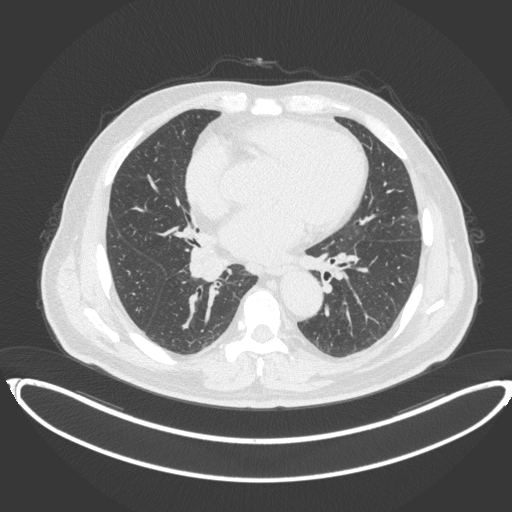
Chest CT, one axial slice. Position 192 of 383 along the scan axis. Reconstruction kernel B31f. 120 kVp. Lung window (W 1500 / L -600 HU). 1 mm slice thickness. 512 × 512 image matrix, field of view 448 × 448 mm. Male patient, age 61 years. From the clinical record (not read from this slice): clinical TNM (as recorded): T1b N1 M0.
Annotated regions visible in this slice (rectangle marked by the reading radiologist):
- lung tumour (recorded histology: squamous cell carcinoma): bounding box <185,243,229,286> (left, top, right, bottom; pixels)